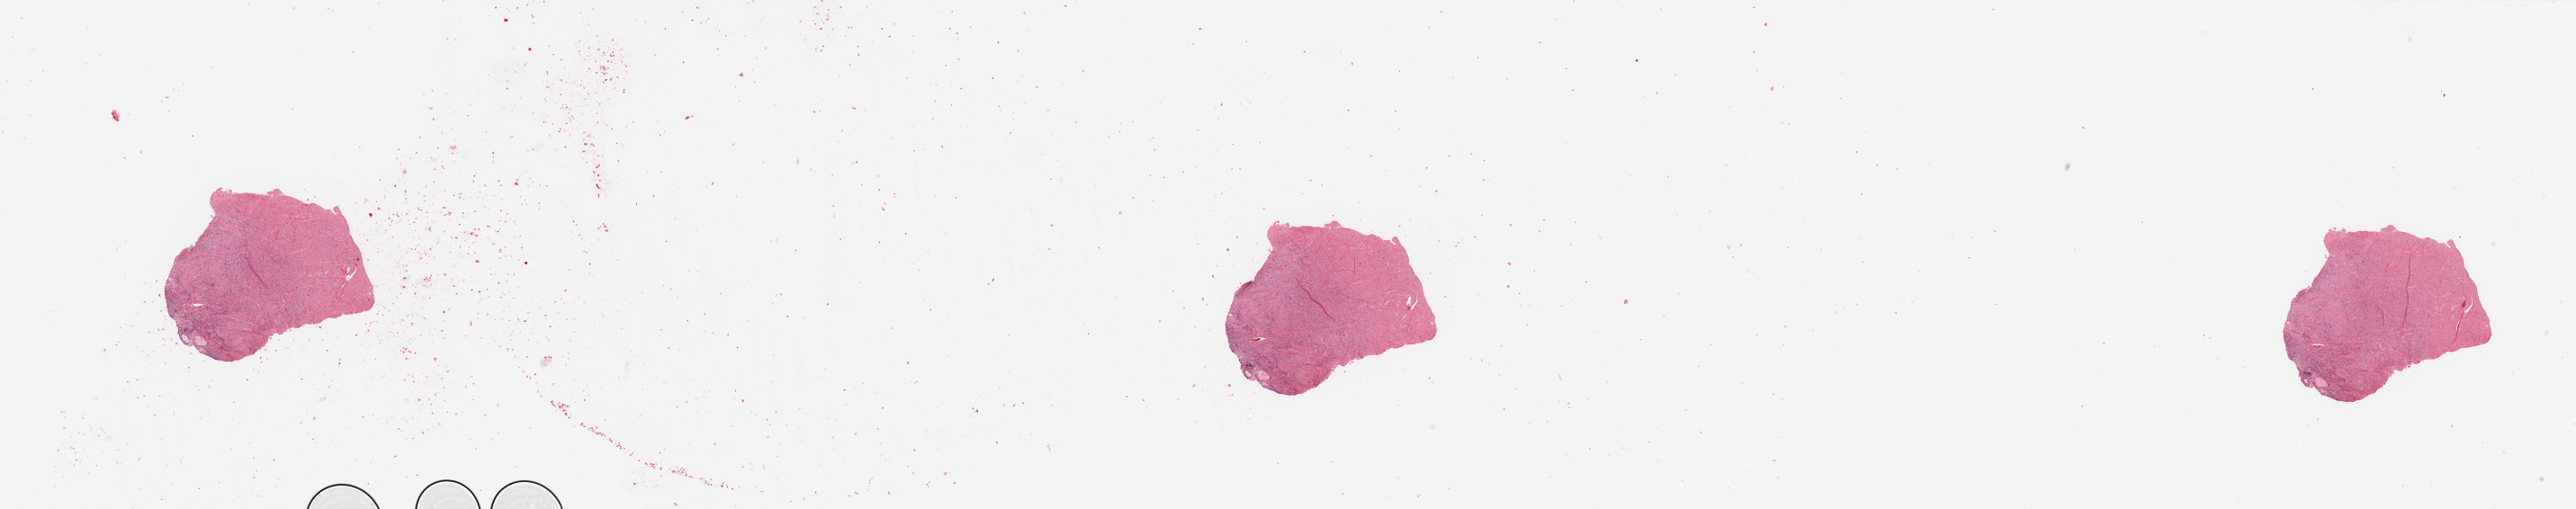
H&E whole-slide image, whole scanned area (about 45.3 x 9.0 mm, slide scanned at 20x) shown as a low-resolution overview; normal (non-tumour) tissue sample, uterus. Patient: female, age 85 years.
This section: normal (non-tumour) tissue from the same patient. Patient diagnosis: Endometrioid adenocarcinoma, NOS.